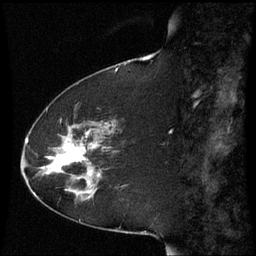
Breast MRI (dynamic contrast-enhanced), one sagittal slice. Dynamic contrast-enhanced series, image 2 of 3 at this slice position (ordered by acquisition). 1.5 T. TE 4.2 ms, TR 8.9 ms. 2.3 mm slice thickness. 256 × 256 image matrix, field of view 210 × 210 mm. Patient: female, 51 years. From the clinical record (not read from this slice): setting: breast cancer imaged before/during neoadjuvant chemotherapy; receptor status: HR-positive, HER2-negative.
Annotated regions visible in this slice (semi-automatic segmentation, software-assisted and operator-edited):
- analysis volume of interest (the breast-tissue region the enhancement analysis was run in; not a lesion): box from (x=50, y=122) to (x=117, y=187) px
- tumour enhancement mask (voxels above the 70 % enhancement threshold inside the analysis volume of interest): (x=53, y=144)–(x=95, y=174)